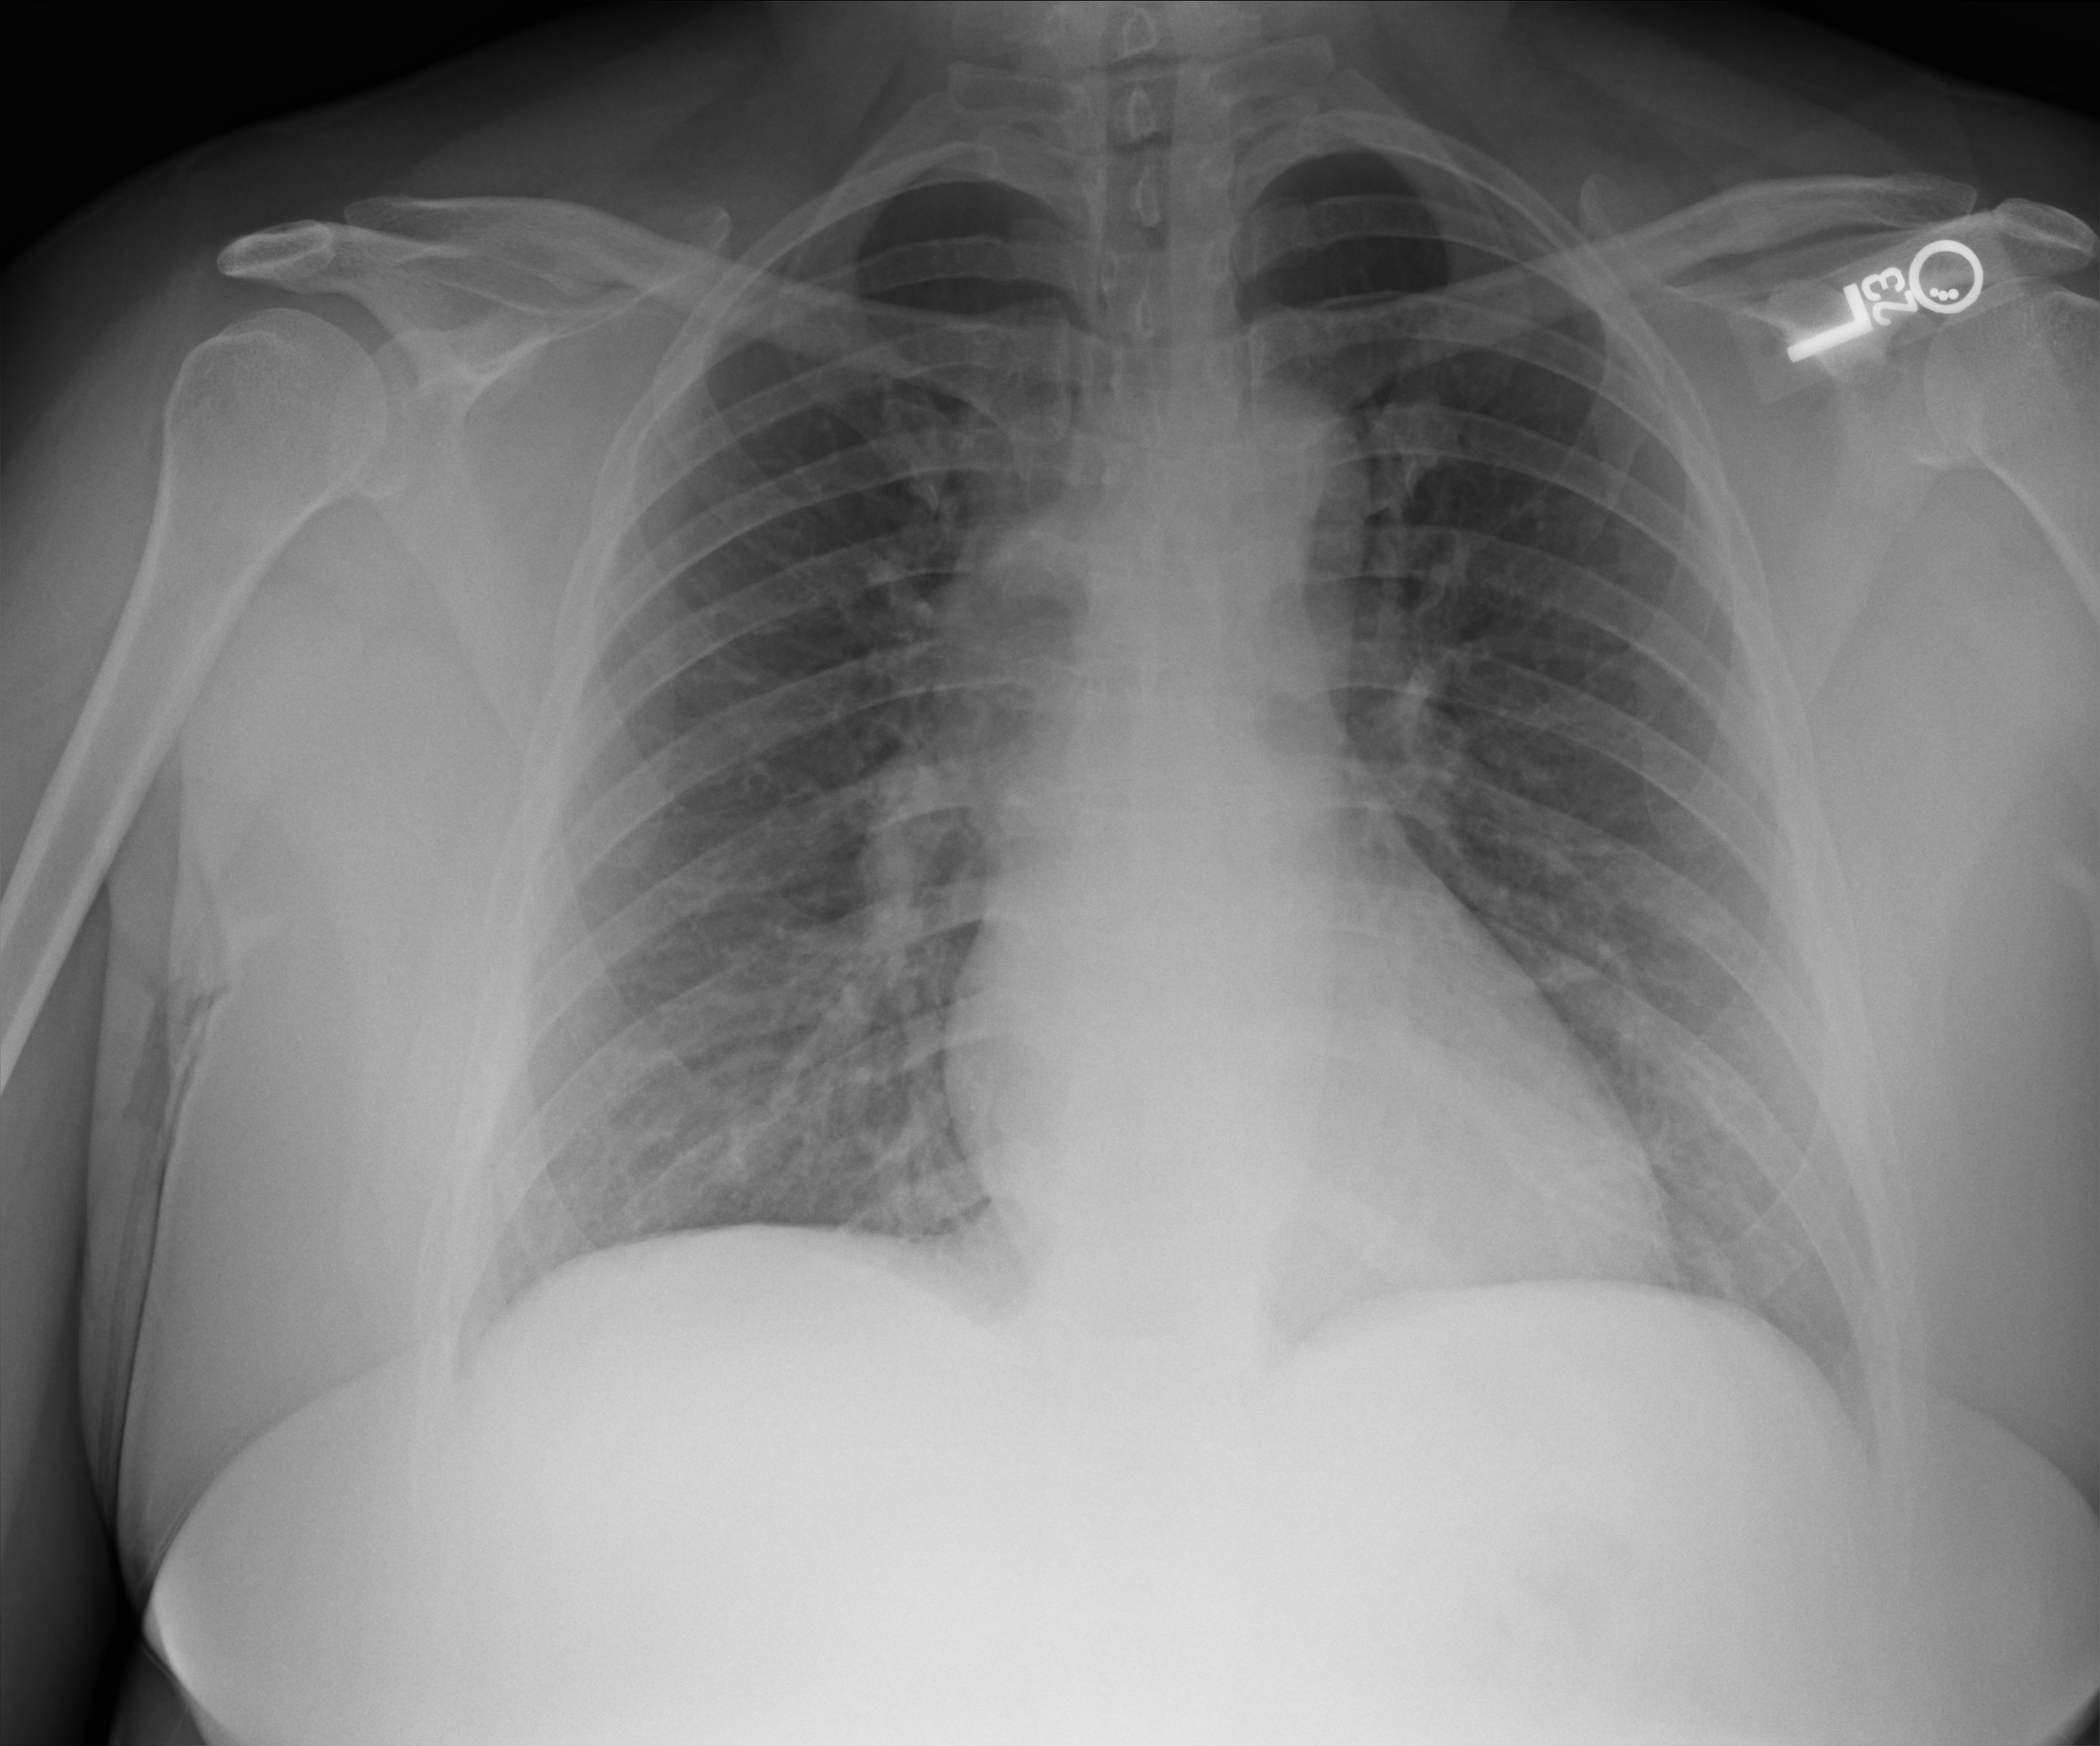
Portable chest radiograph; anteroposterior (AP) projection. Female patient hospitalised with COVID-19, age 18–59 years.
From the hospital-stay record, not from the radiograph (when in the stay this image was taken is not recorded): admitted to intensive care during this hospital stay: no; length of hospital stay: 1 day; diabetes (admission record): no.